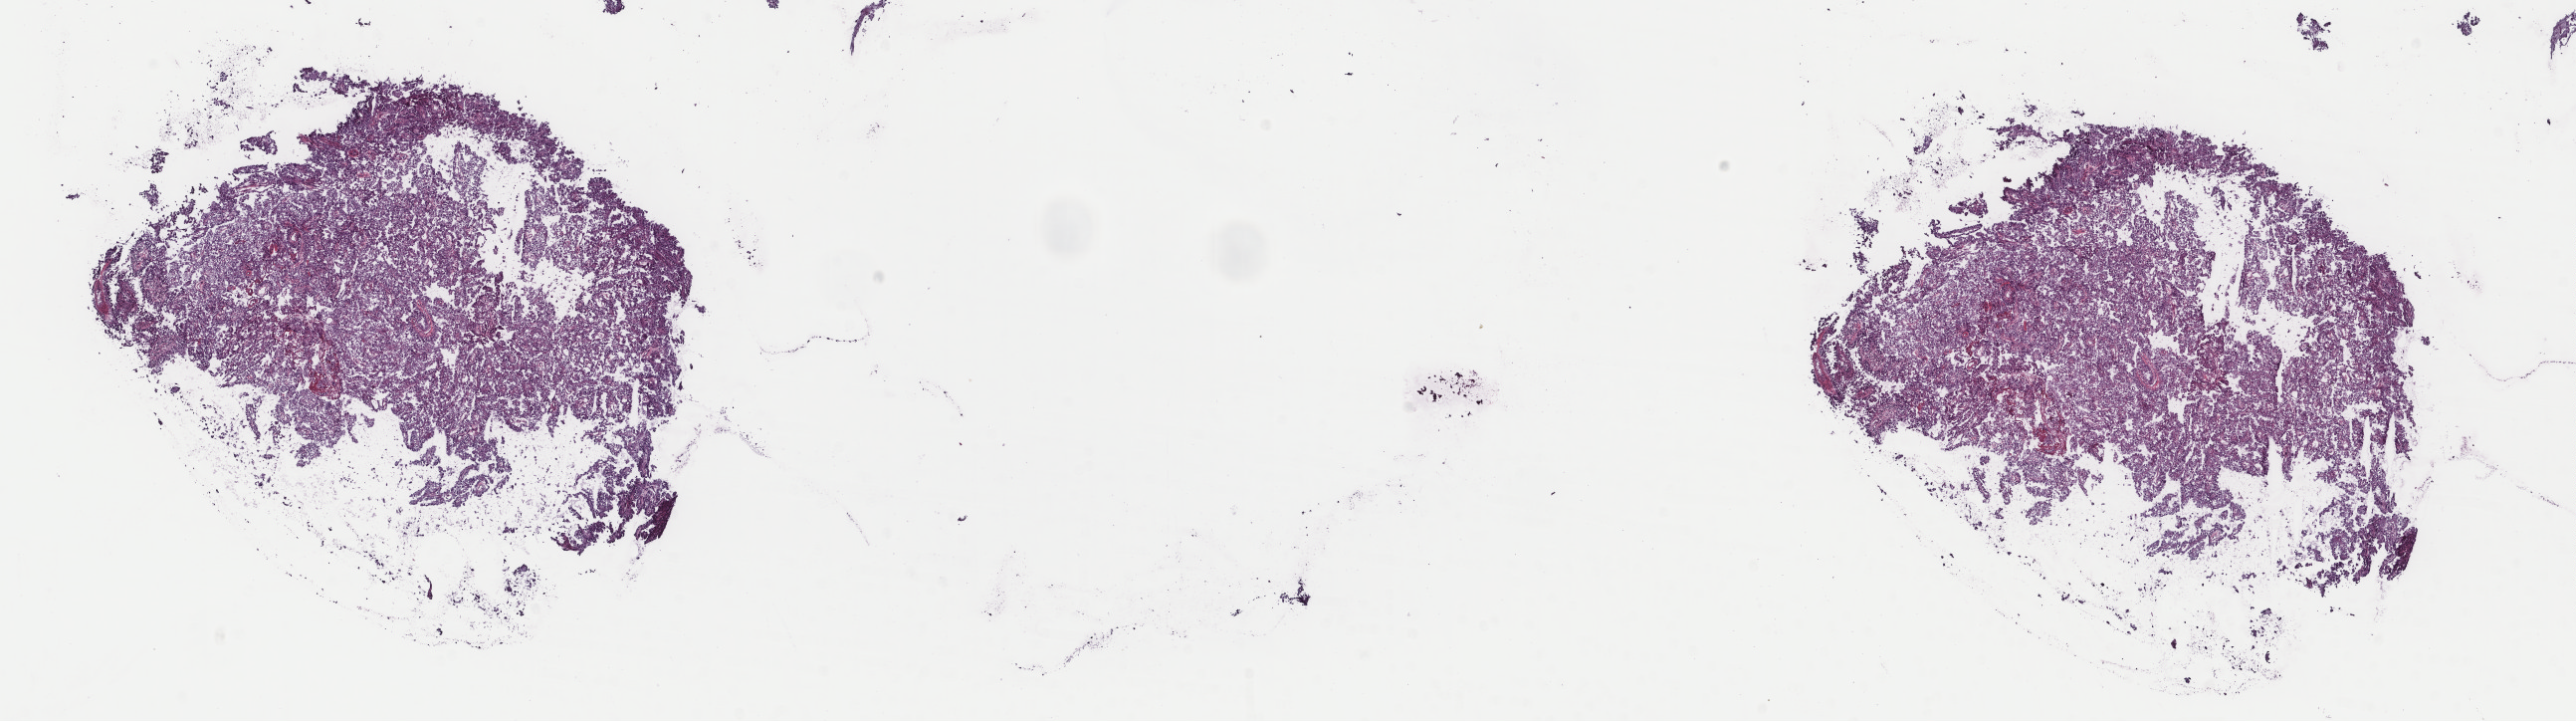
Digitized H&E-stained tissue section (whole slide), low-resolution overview of the scanned area, about 20.5 x 5.7 mm (slide scanned at 40x); frozen section; sample: primary tumour, kidney. Male, age 57 years at initial diagnosis. Composition of this section per pathologist review: tumour cells 90%, tumour nuclei 90%, normal cells 0%, stromal cells 10%, necrosis 0%. Inflammatory infiltration, as recorded: lymphocyte infiltration 0%, monocyte infiltration 0%, neutrophil infiltration 0%.
TNM: T2a N1 M0. Laterality: left. Lymph nodes positive (case pathology): 4 of 4 examined. AJCC pathologic stage: III (7th edition). Pathologic diagnosis: Papillary adenocarcinoma, NOS.